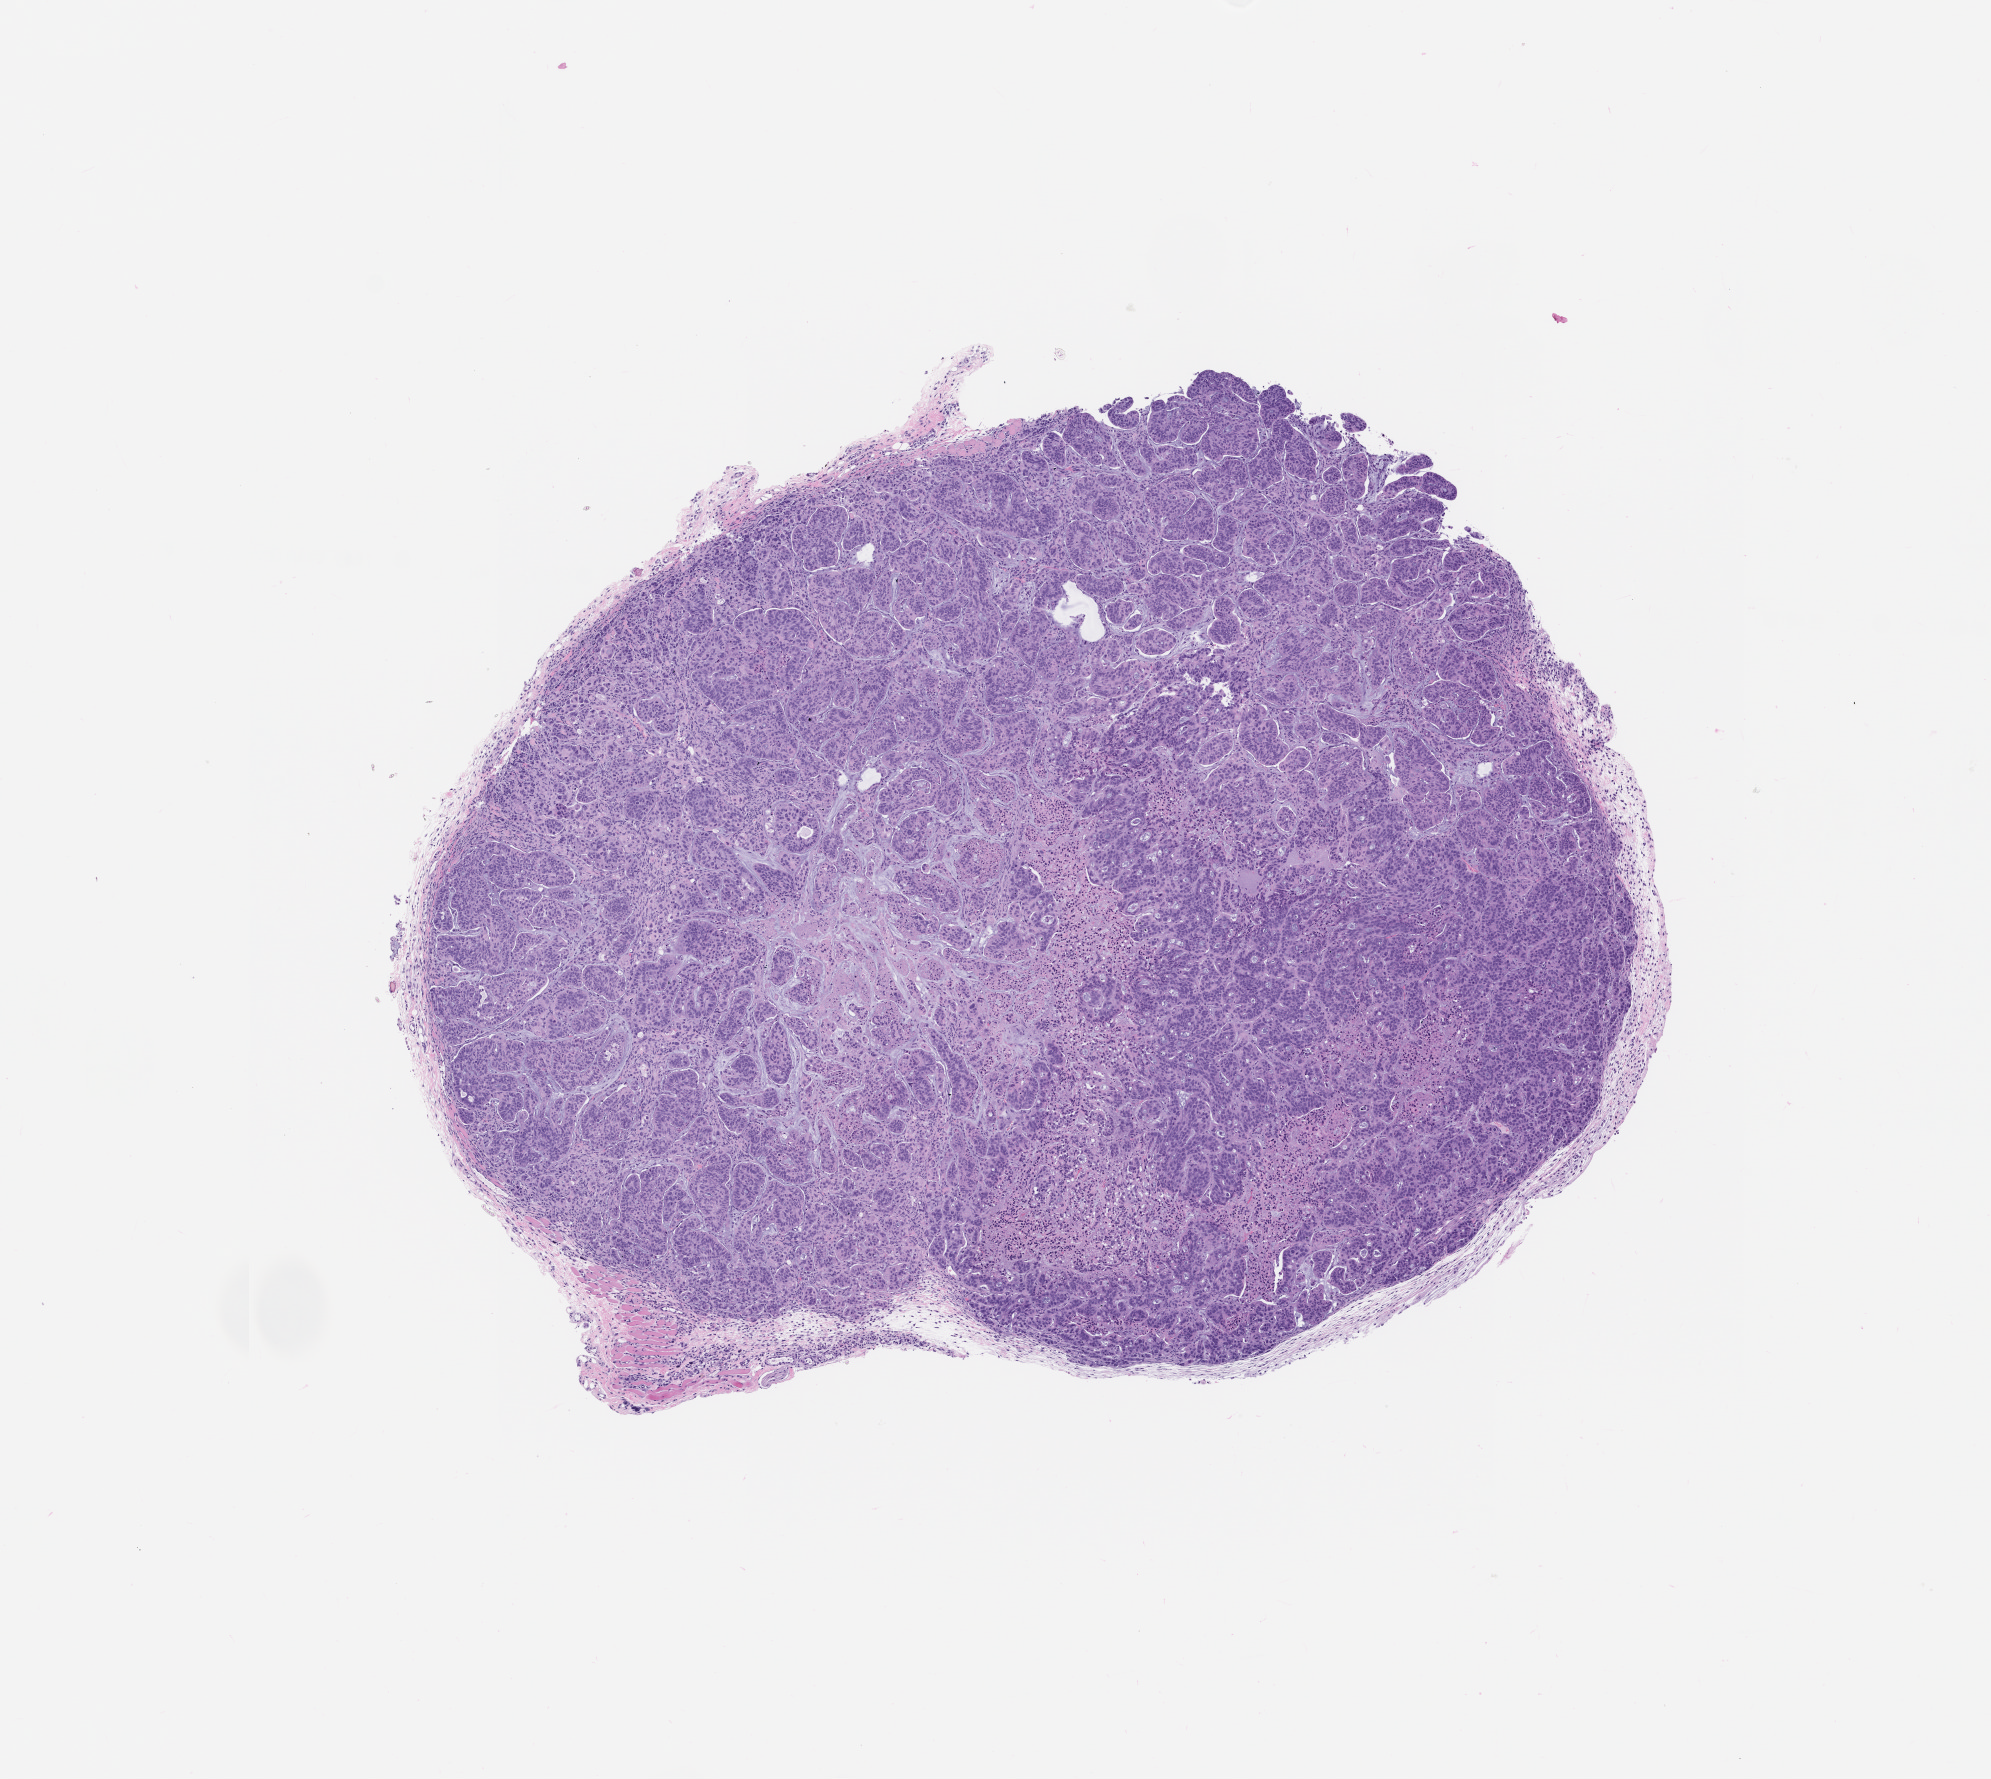
Haematoxylin and eosin whole-slide image of a patient-derived xenograft (PDX) tumor grown in a mouse, passage 2, whole scanned area (about 8.0 x 7.1 mm) shown as a low-resolution overview, formalin-fixed, paraffin-embedded (FFPE) tissue, tumor site category: small intestine.
• originating patient diagnosis: Small Intestinal Adenocarcinoma